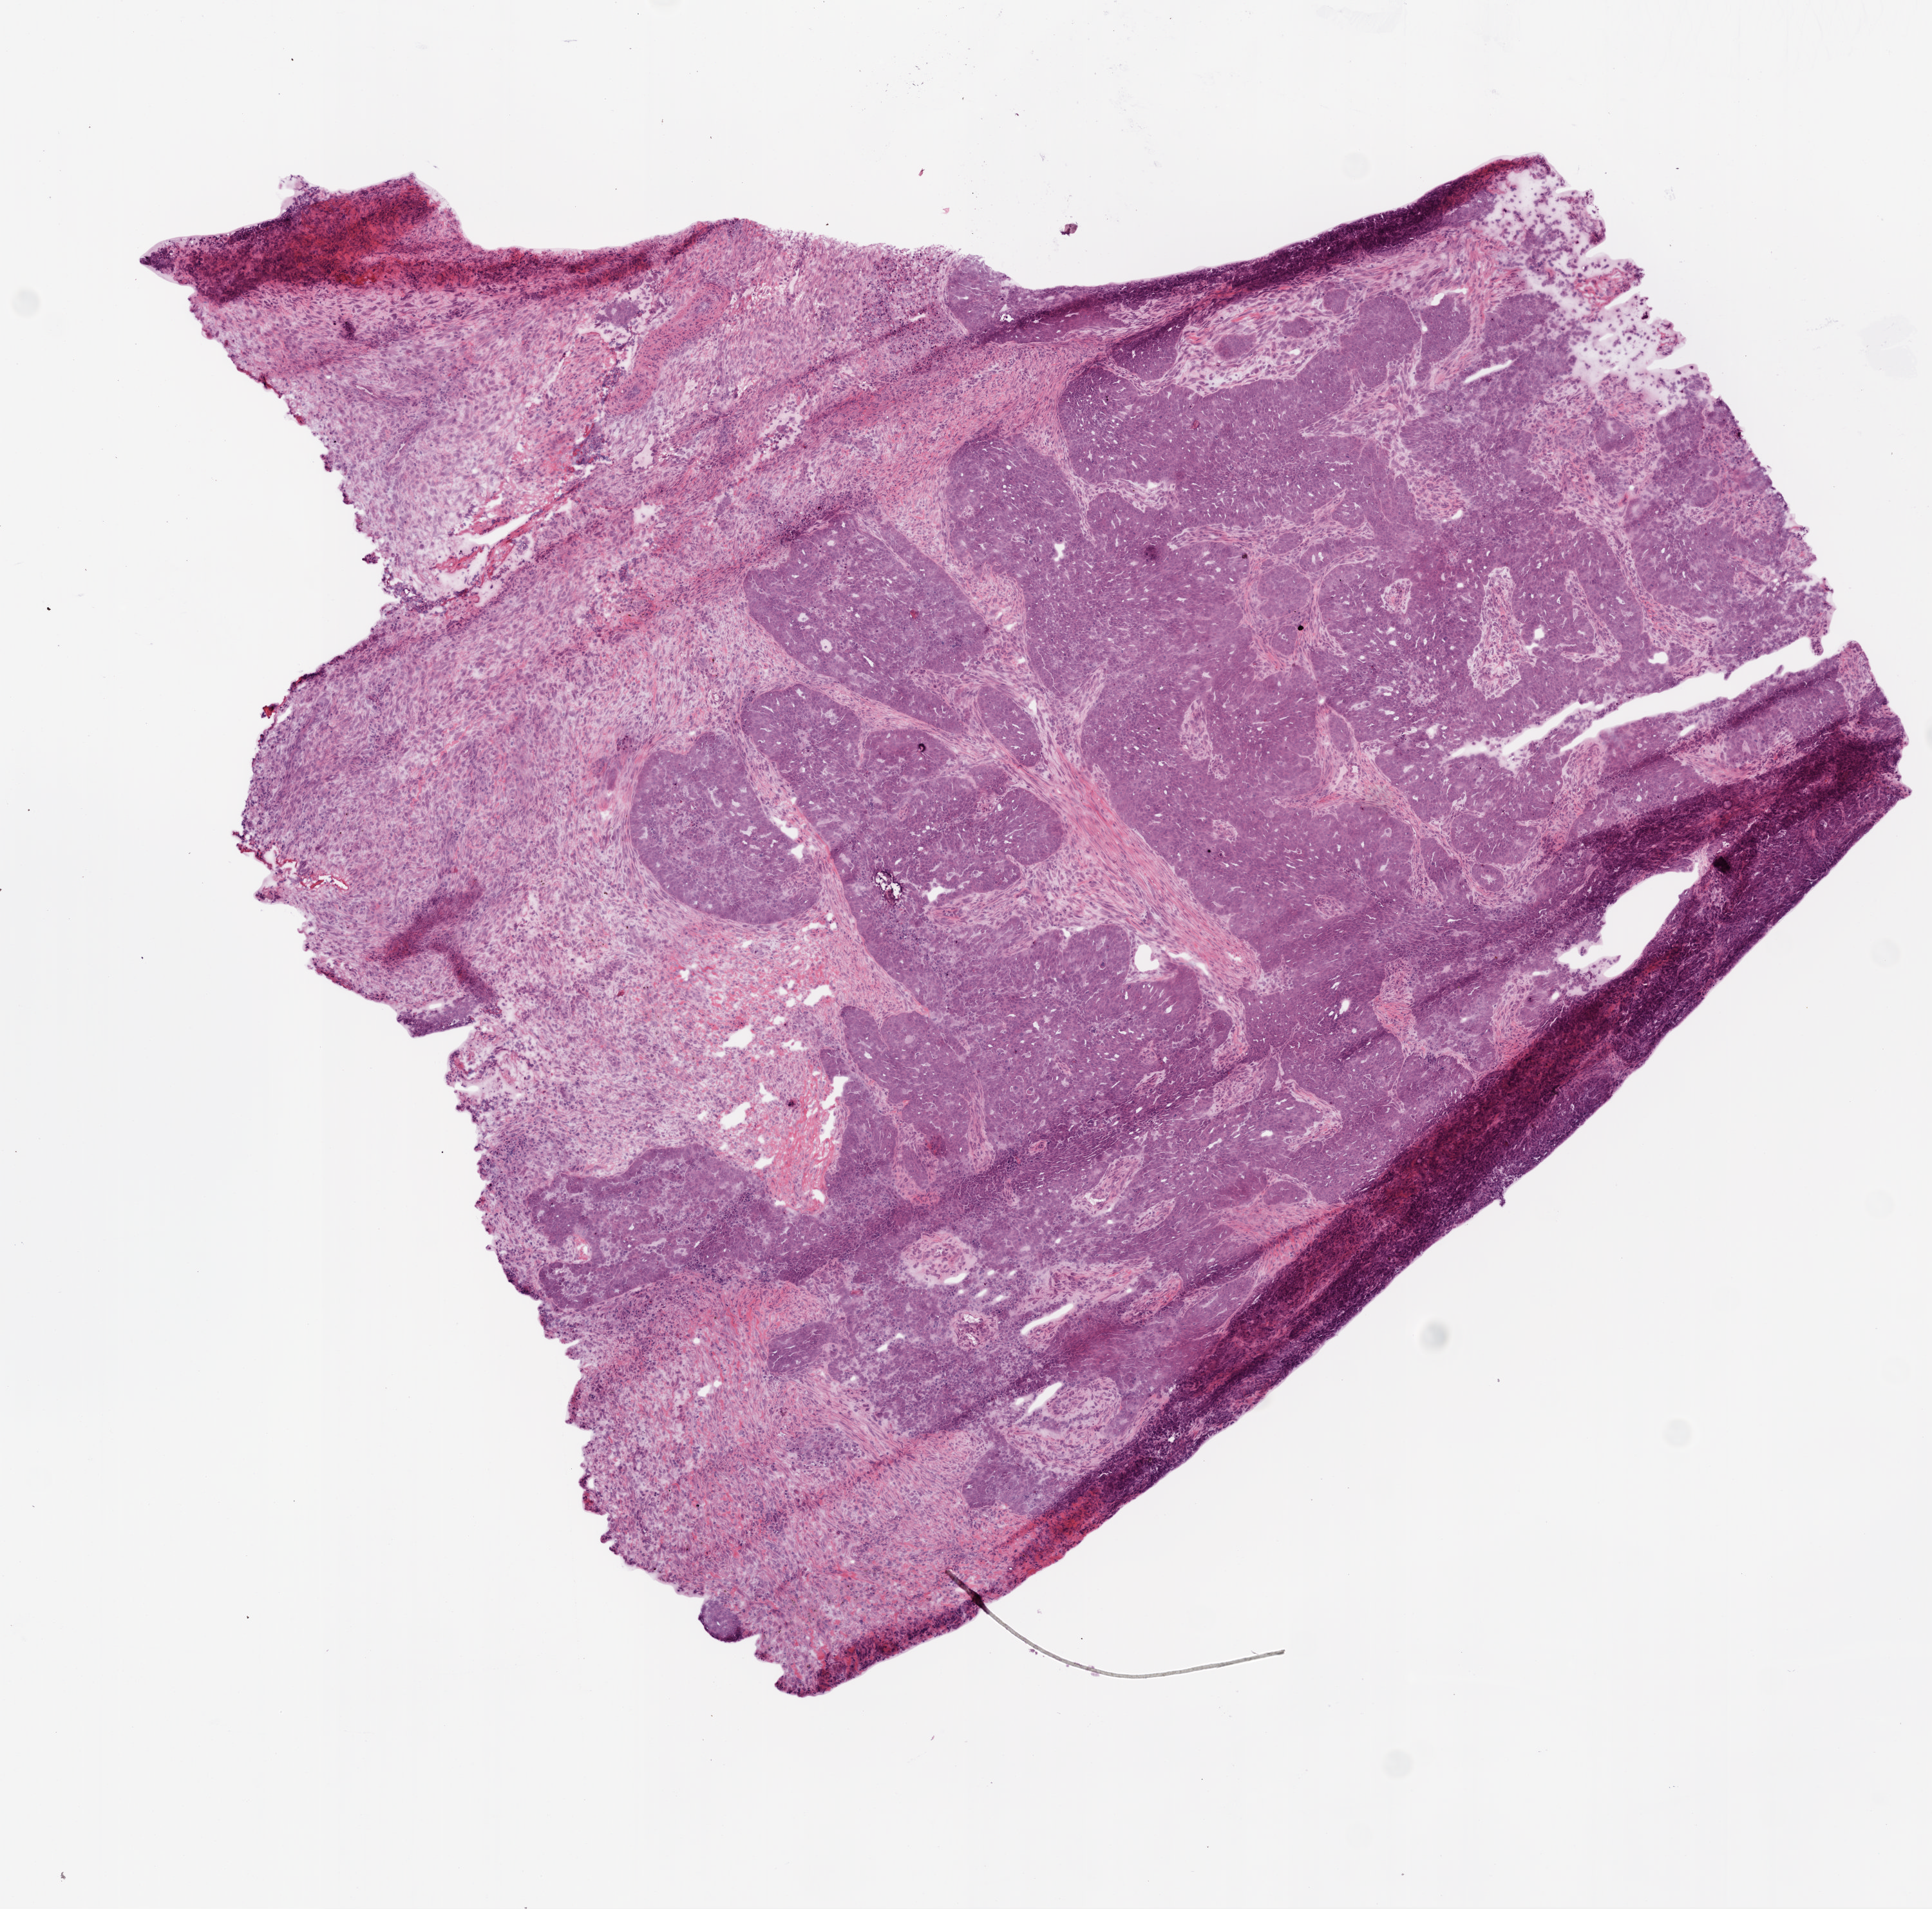
Hematoxylin and eosin (H&E) stained whole-slide image — low-resolution overview of the scanned area, about 6.0 x 5.9 mm (slide scanned at 20x). Frozen section from the top of the tissue portion. Sample: primary tumour, ovary. Female patient; age at initial diagnosis 48 years. Histologic grade: G3 (poorly differentiated). Slide review estimates, as recorded: tumour cells 80%, tumour nuclei 80%, normal cells 0%, stromal cells 20%, necrosis 0%.
FIGO stage: IIIC. Histologic diagnosis: Serous cystadenocarcinoma, NOS.